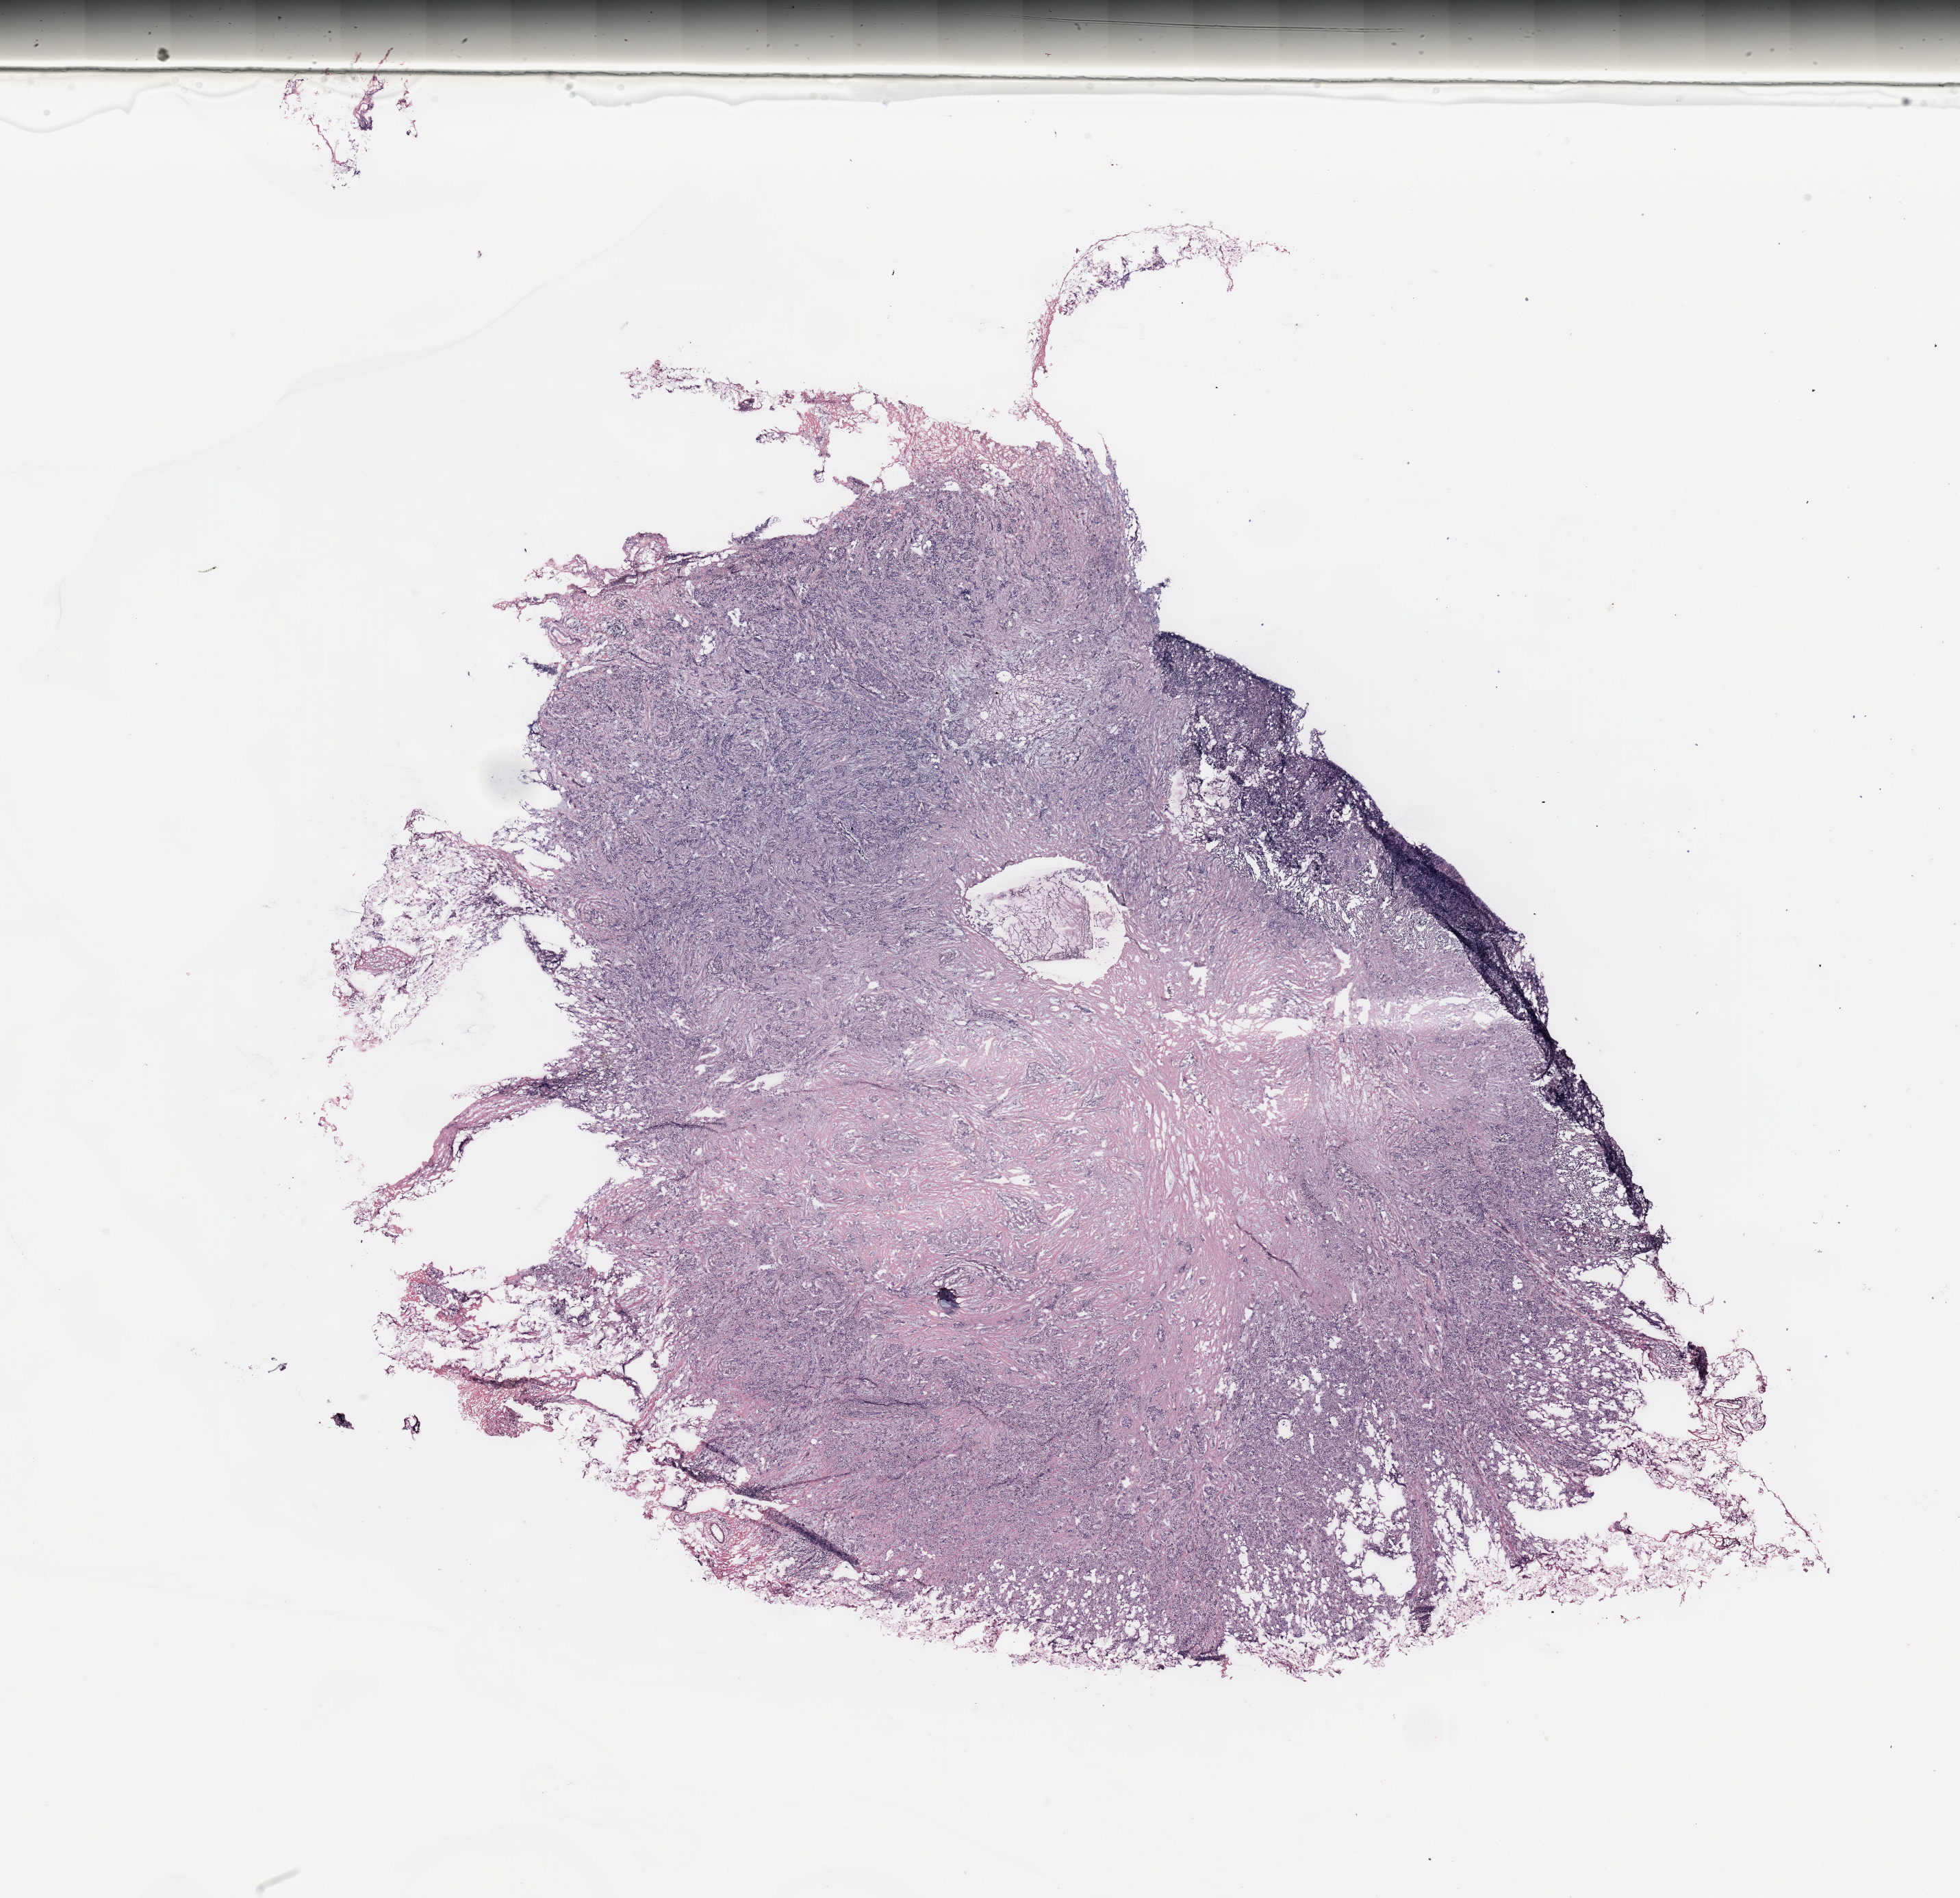
Digitized H&E-stained tissue section (whole slide) — low-resolution overview of the scanned area, about 22.6 x 21.9 mm (acquisition: 20x scan); breast, tumour tissue. 65-year-old female patient.
• AJCC pathologic stage: IIA
• diagnosis: Infiltrating duct carcinoma, NOS